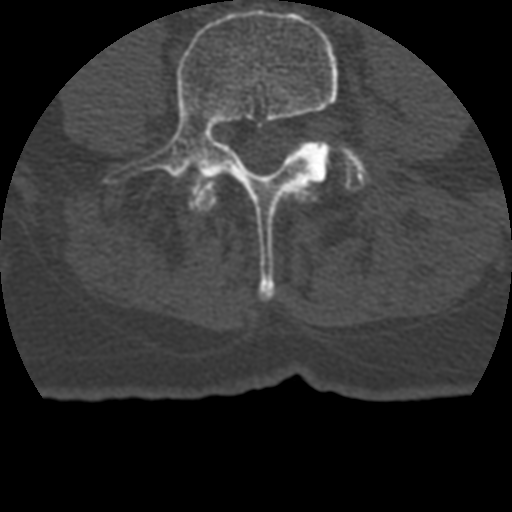
CT including the spine, one axial slice; position 66 of 399 along the scan axis; reconstruction kernel STANDARD; 120 kVp; bone window (W 1800 / L 400 HU); 1.25 mm slice thickness; 512 × 512 image matrix. Patient age 69 years. From the clinical record (not read from this slice): primary cancer: prostate.
Annotated regions visible in this slice (semi-automatic segmentation, software-assisted and operator-edited):
- L3 vertebra: bounding box (x1, y1, x2, y2) in pixels: (194, 180, 317, 212)
- L4 vertebra: (105, 9, 338, 300)
- L5 vertebra: (333, 148, 368, 190)